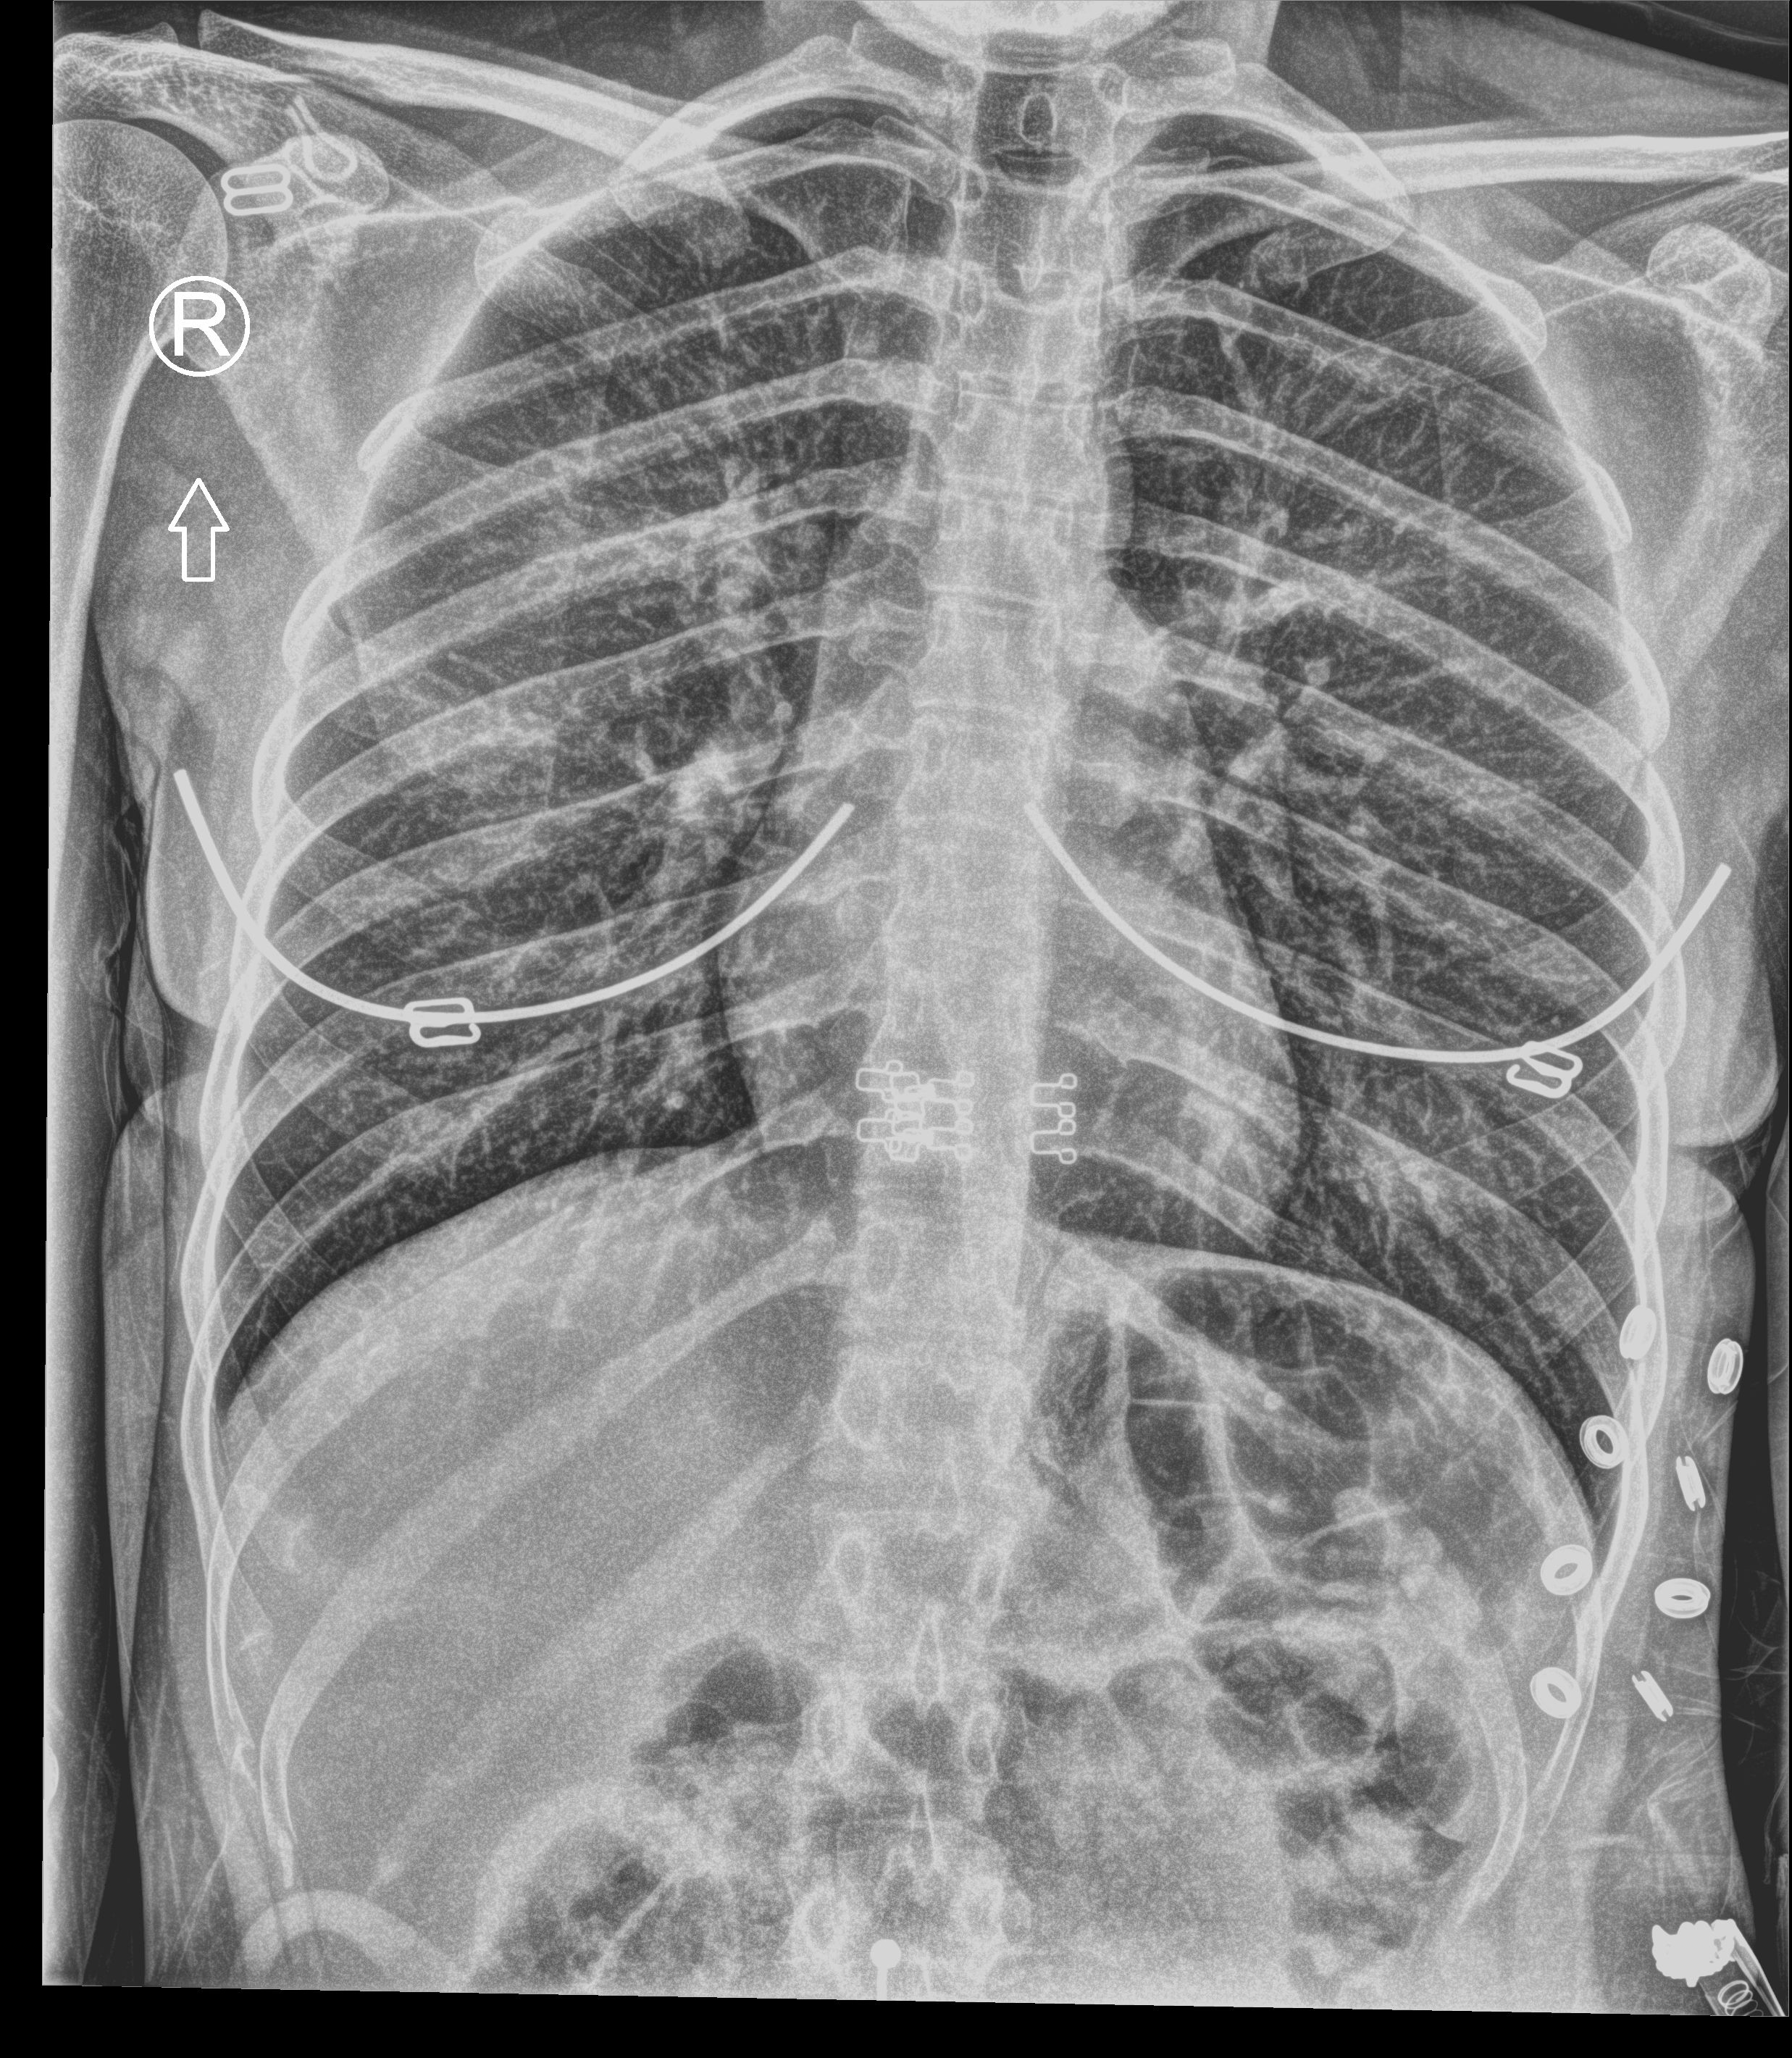
Portable chest radiograph, anteroposterior (AP) projection. Patient hospitalised with COVID-19; female, aged 18–59 years.
From the hospital-stay record, not from the radiograph (when in the stay this image was taken is not recorded): mechanically ventilated during this hospital stay: no; hypertension (admission record): no; admitted to intensive care during this hospital stay: no.